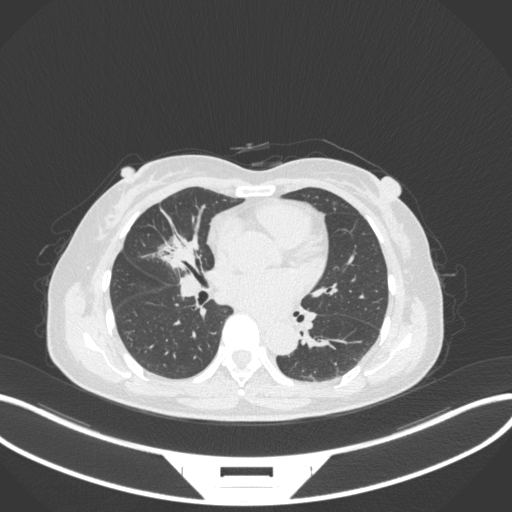
Chest CT, one axial slice. Reconstruction kernel B31f. 120 kVp. Lung window (W 1500 / L -600 HU). 1 mm slice thickness. 512 × 512 image matrix, field of view 400 × 400 mm. Female patient, age 51 years. From the clinical record (not read from this slice): clinical TNM (as recorded): T1c N0 M0.
Annotated regions visible in this slice (rectangle marked by the reading radiologist):
- lung tumour (recorded histology: adenocarcinoma): bounding box [x1, y1, x2, y2] px = [153, 227, 202, 271]